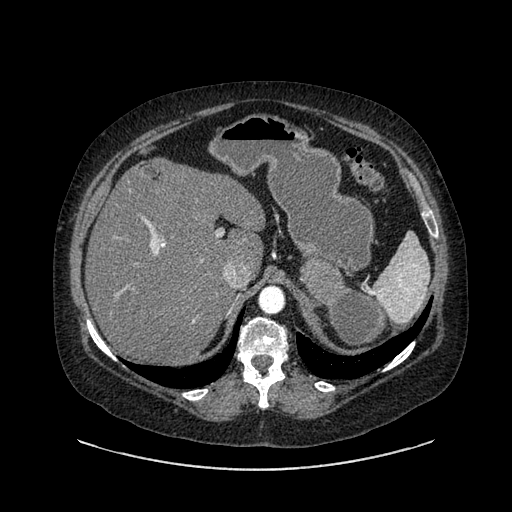
Contrast-enhanced abdominal CT, one axial slice; slice 622 of 769 in the series (ordered by position); reconstruction kernel SOFT; intravenous contrast given; soft-tissue window (W 400 / L 40 HU); 512 × 512 image matrix, field of view 460 × 460 mm. Patient: female, 61 years. Case-level facts recorded for this patient, not image findings: diagnosis: adrenocortical carcinoma; tumour side: left adrenal; tumour size at pathology: 13 cm; Ki-67 index: 79 %.
Outlined on this slice (semi-automatic segmentation, software-assisted and operator-edited):
- mass: bounding box (x1, y1, x2, y2) in pixels: (300, 261, 387, 347)